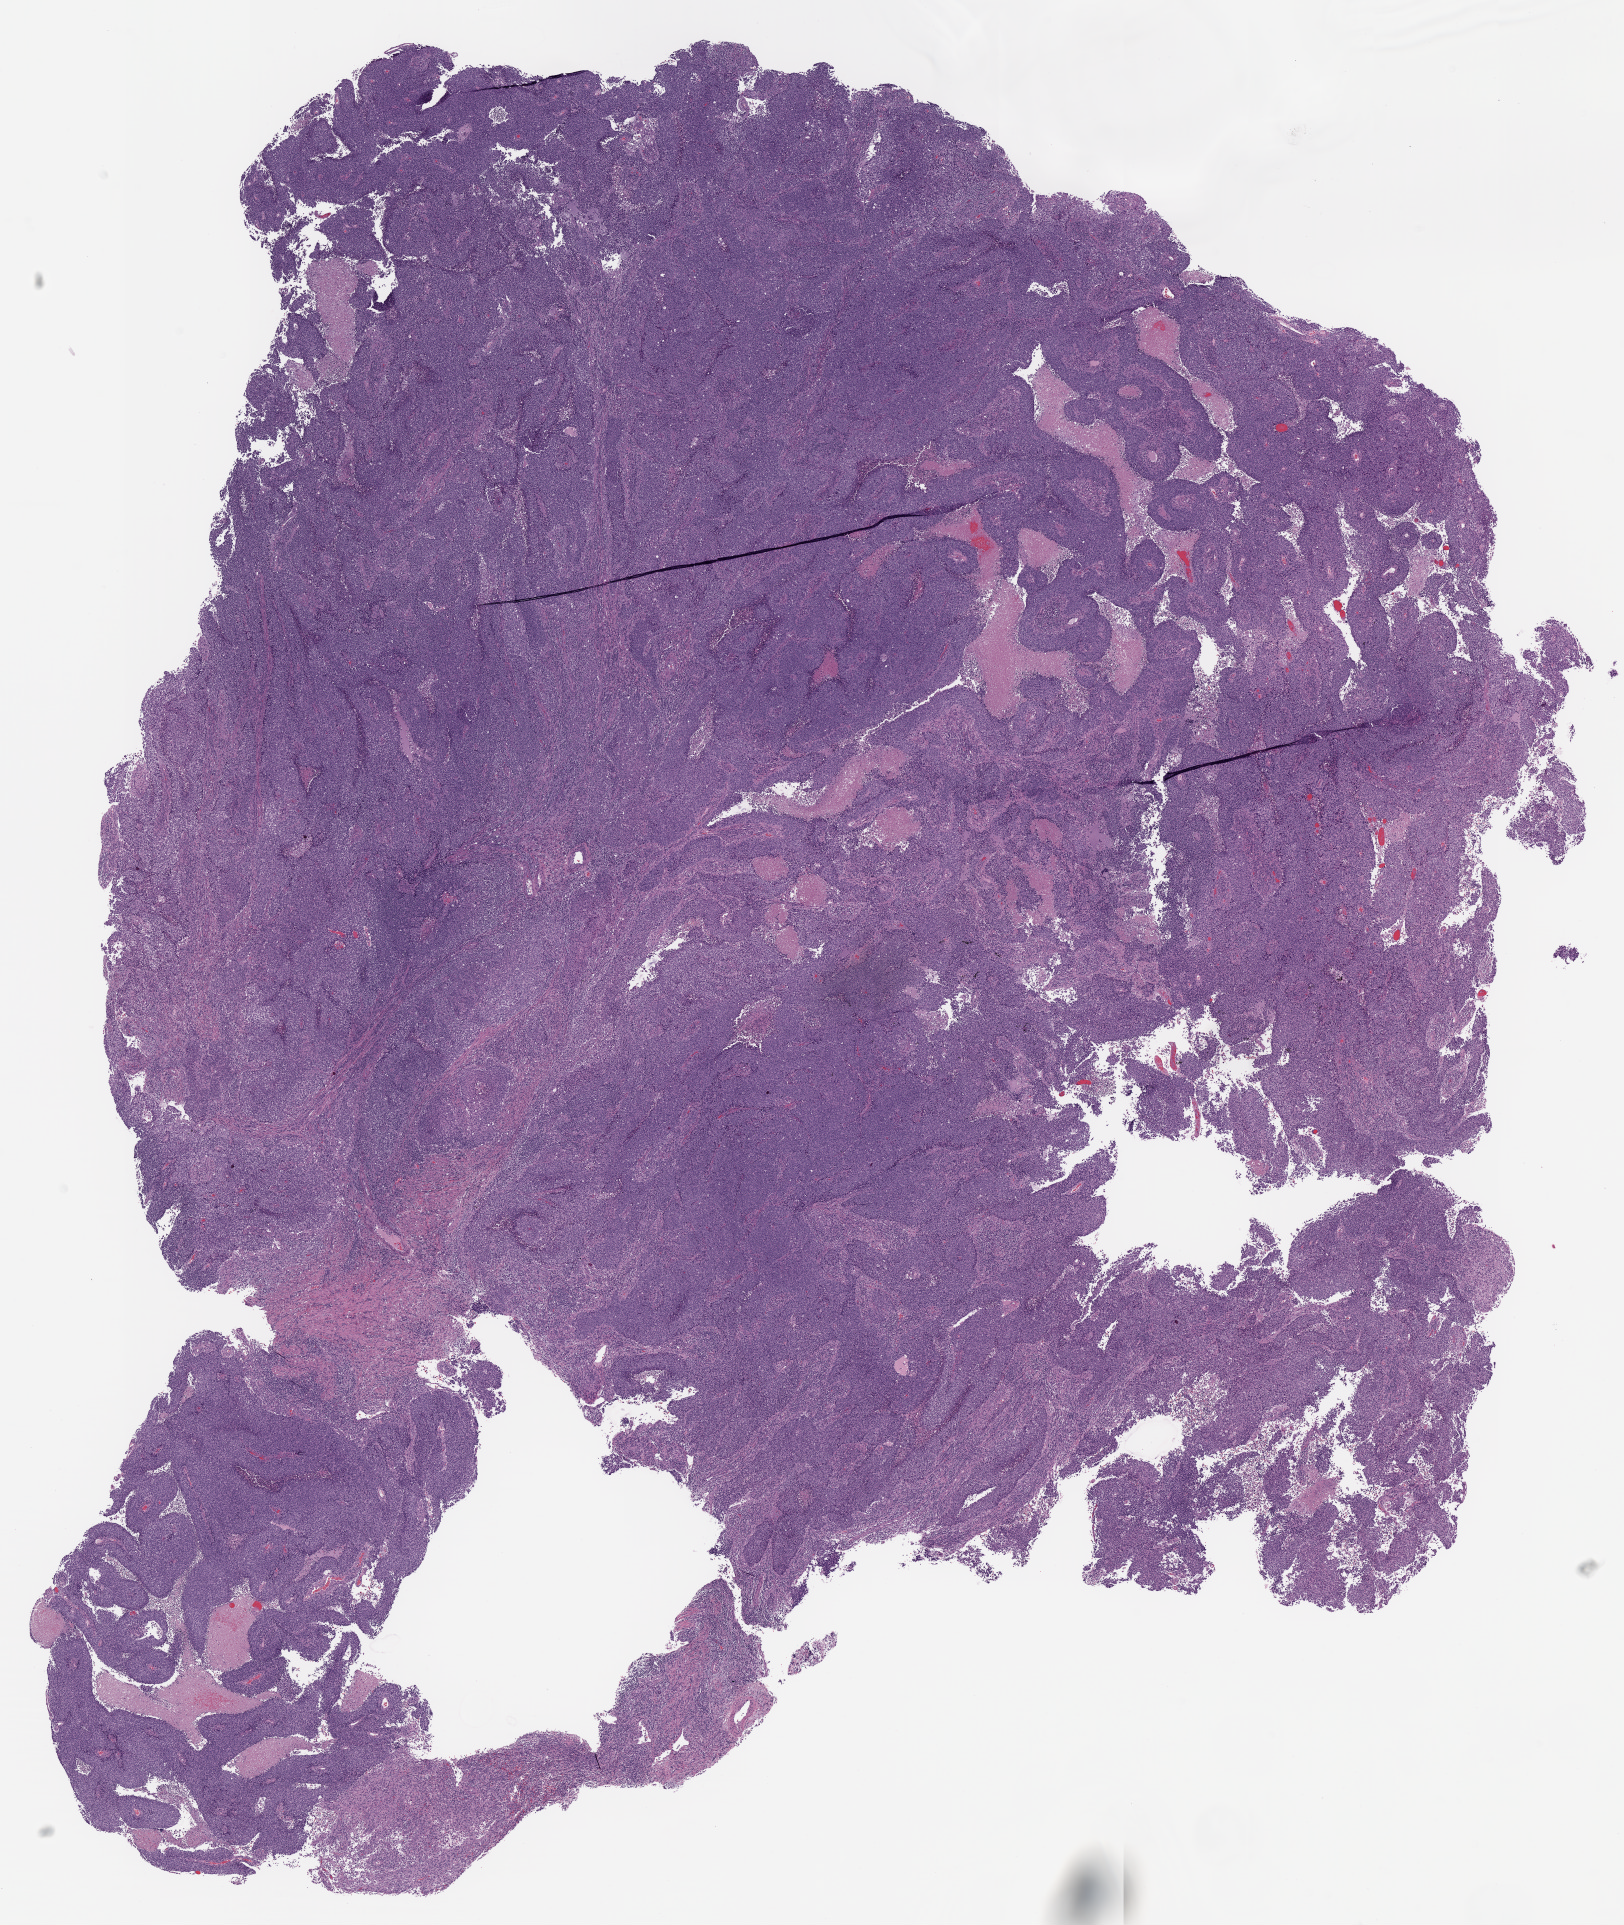
Whole-slide histology image, H&E, a low-resolution overview of the entire scanned area, about 13.0 x 15.4 mm (acquisition: 20x scan); FFPE section; uterus, primary tumour sample. Female patient. Histologic grade: G3 (poorly differentiated).
* FIGO stage: IB
* diagnosis: Endometrioid adenocarcinoma, NOS (endometrium)